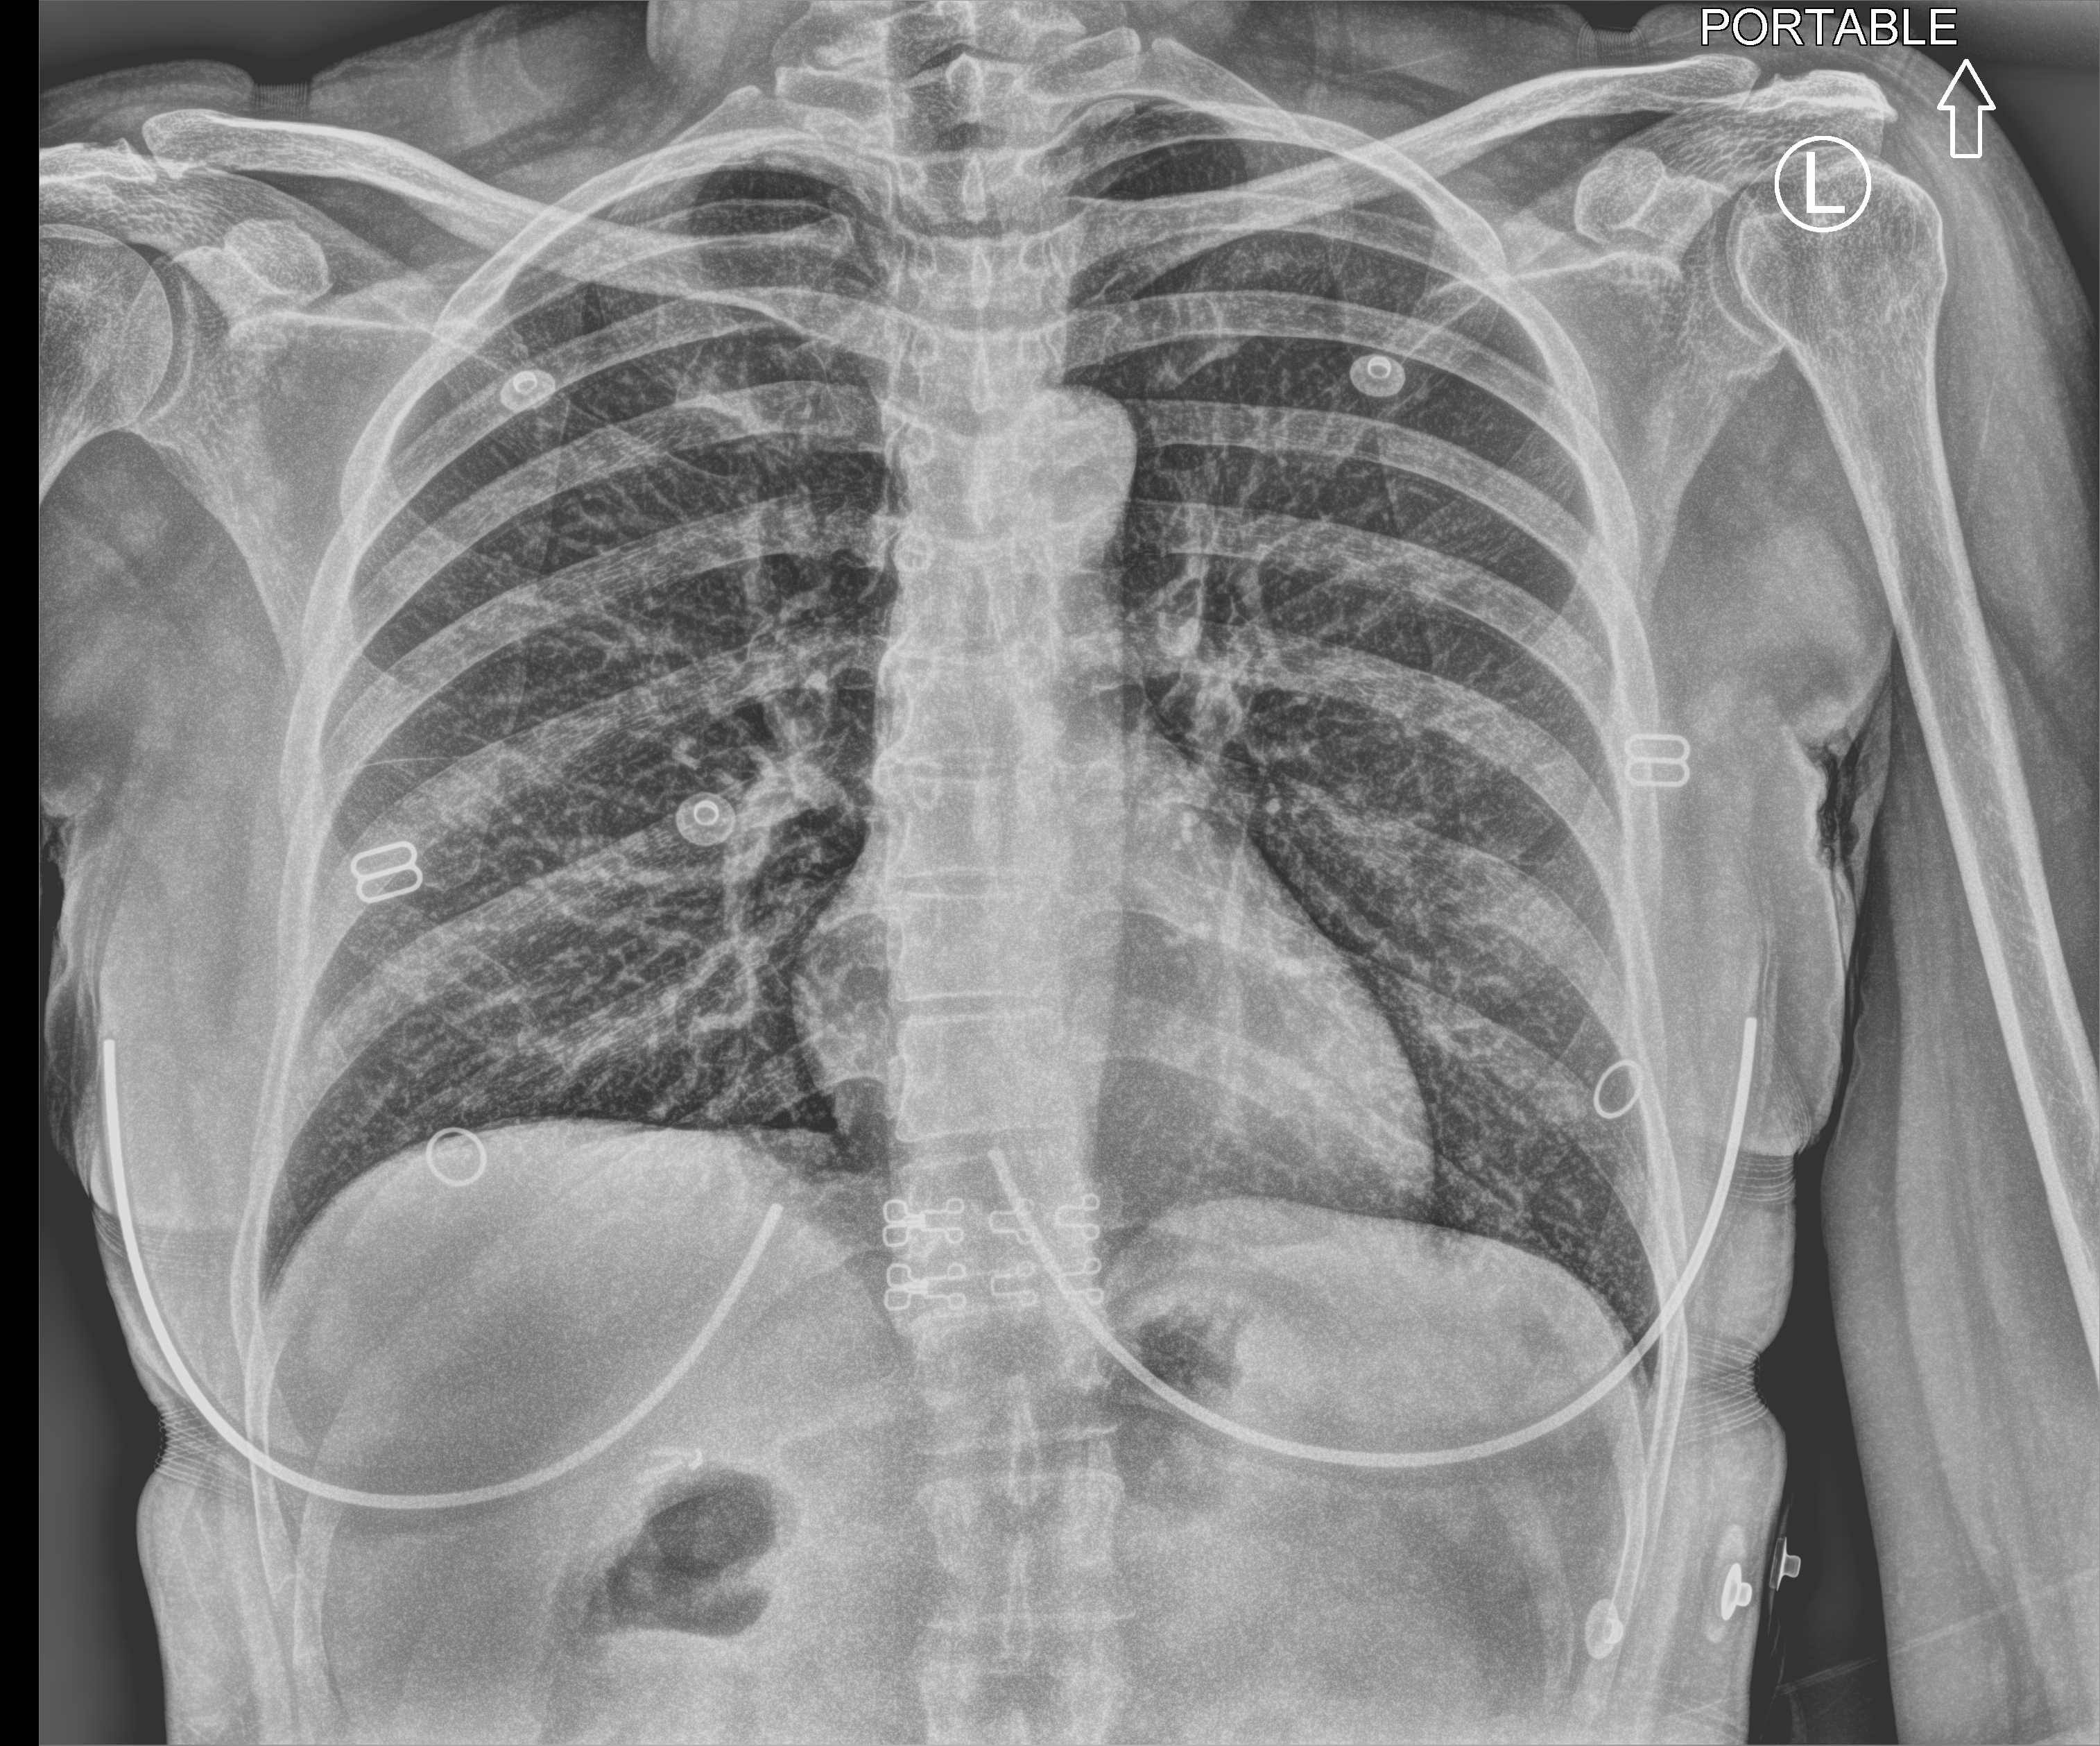
Portable chest radiograph, anteroposterior (AP) projection. Female patient hospitalised with COVID-19, age 18–59 years.
Admission-level facts for this patient (not findings on this image; timing relative to this image not recorded): admitted to intensive care during this hospital stay: no; hypertension (admission record): no.